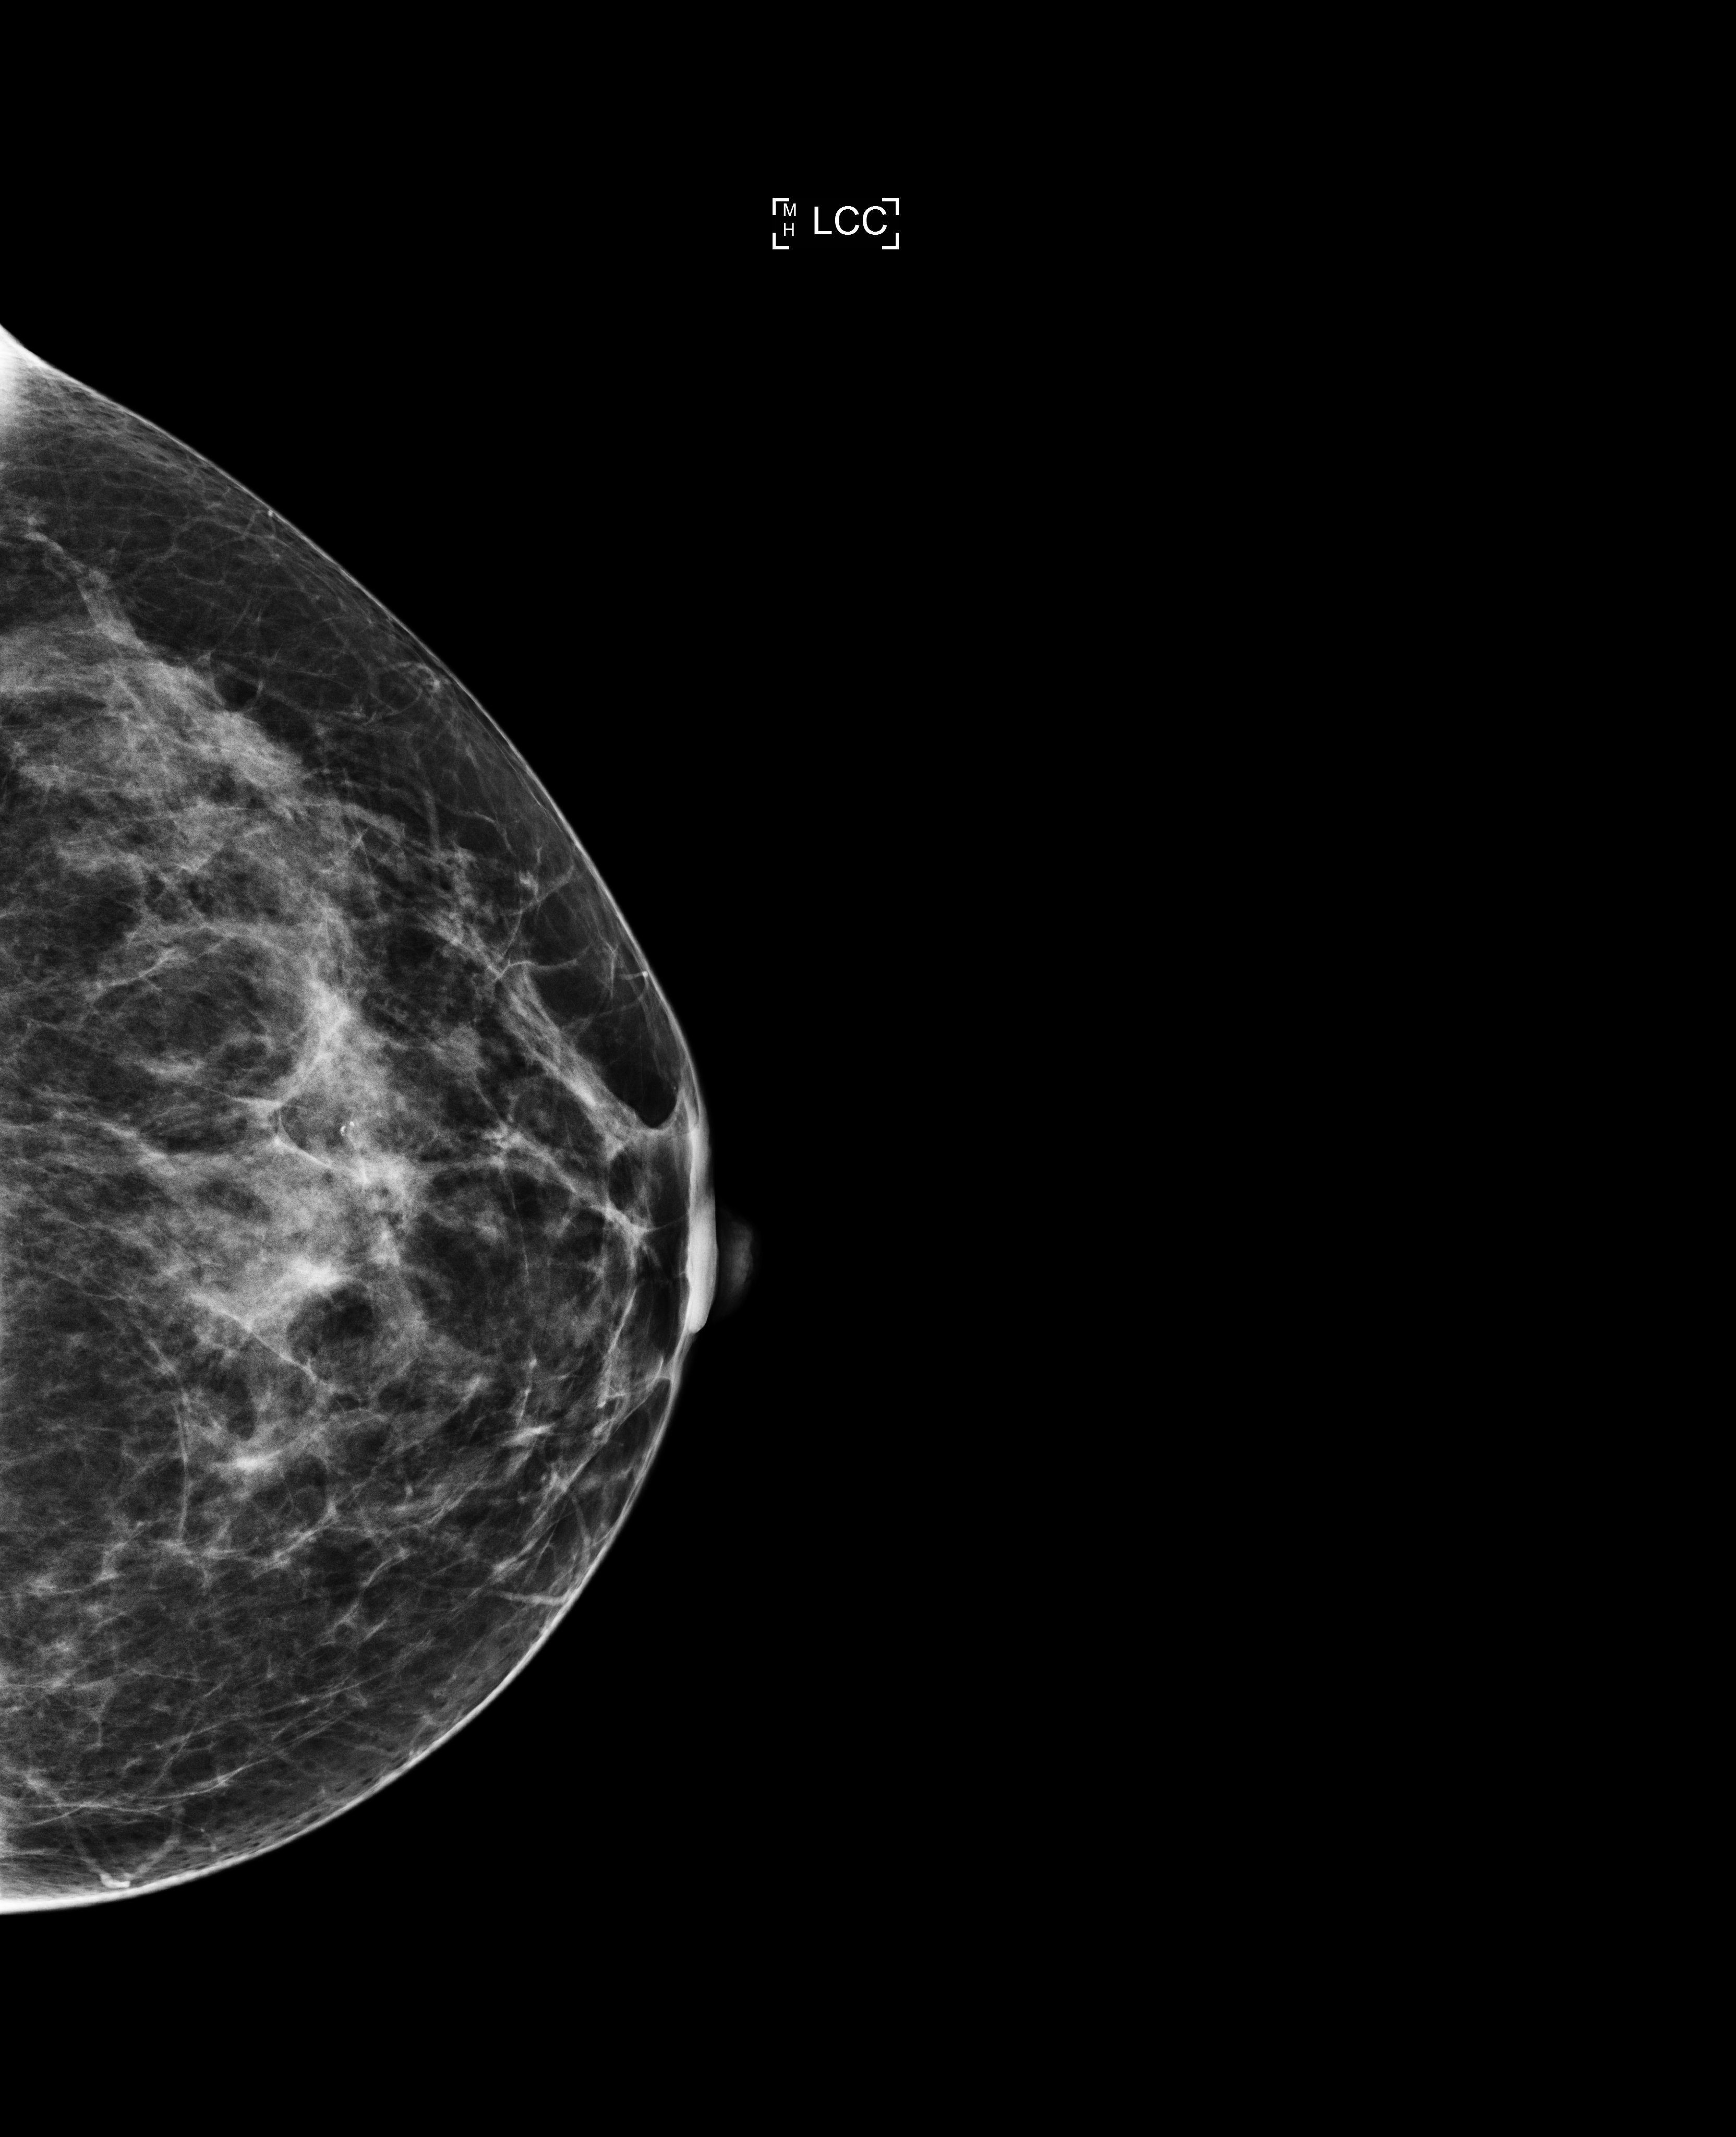
Digital mammogram (FFDM); left breast; cranio-caudal projection; annual screening mammography examination; system: Selenia Dimensions. Female patient, age 46 years.
BI-RADS breast density category at the screening exam (both breasts, scale 1–4): 3. Final BI-RADS assessment for this screening round (tomosynthesis exam, both breasts): category 1. Recall: no recall after this screen.